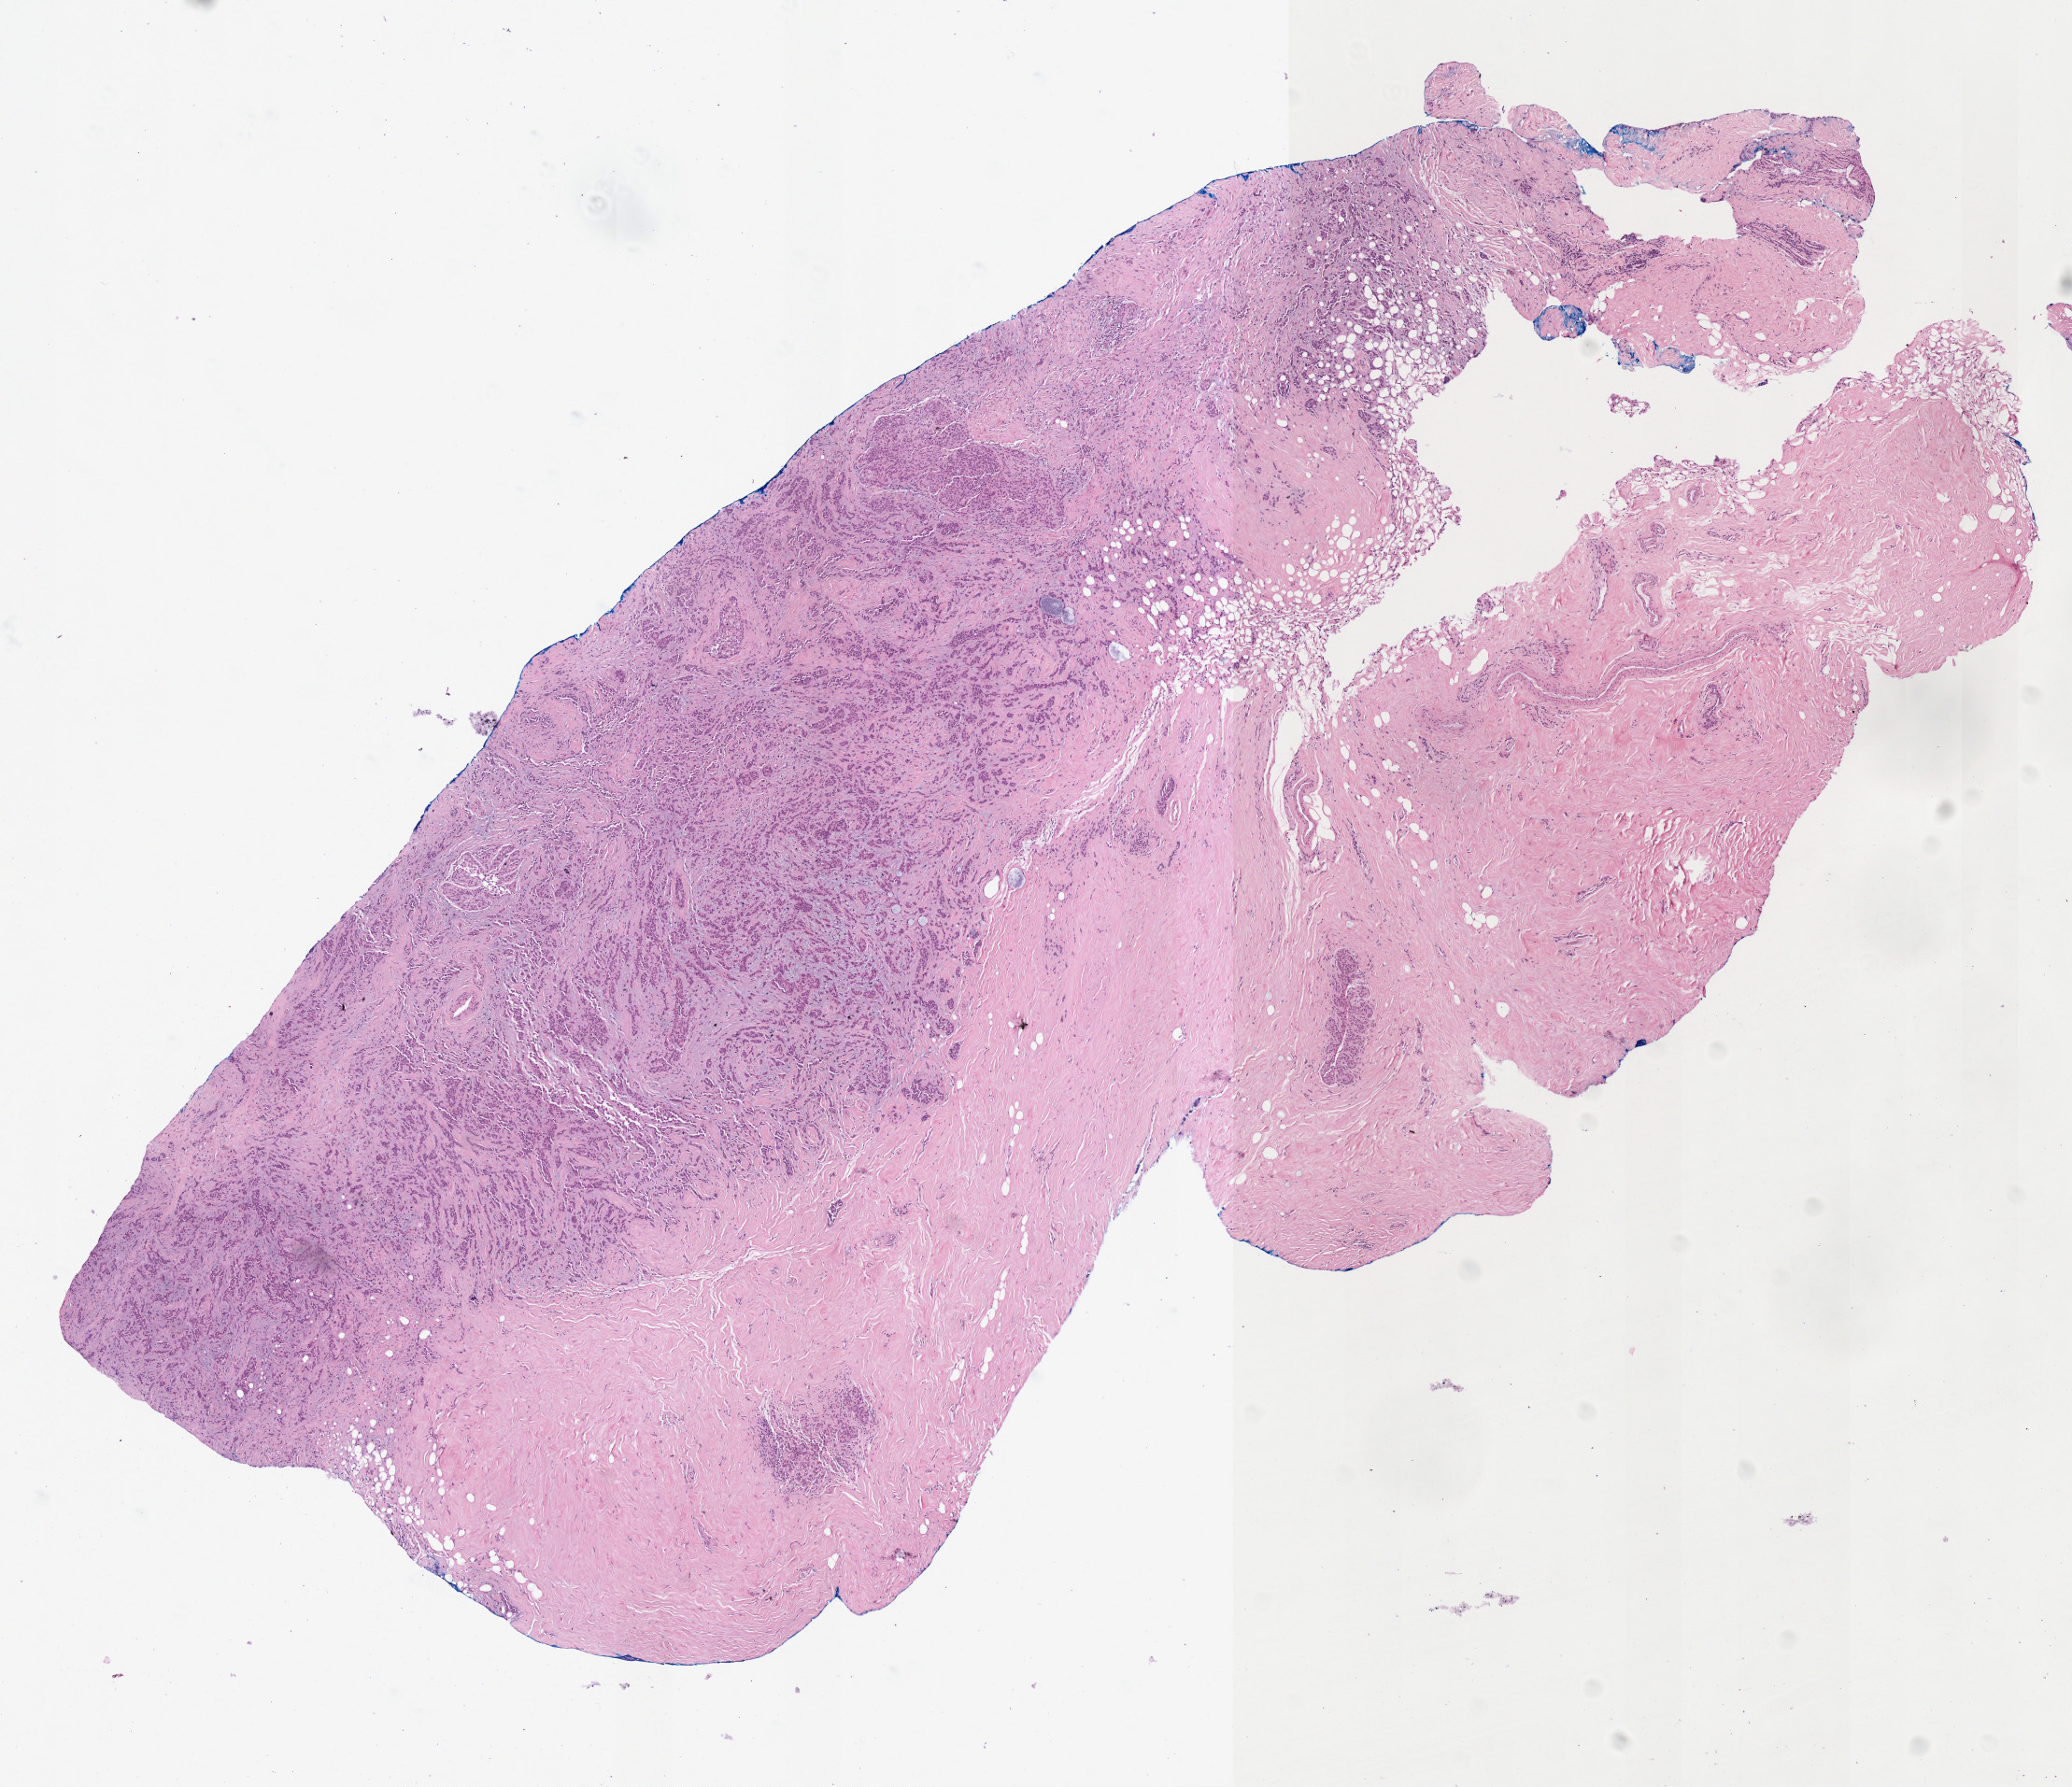
H&E whole-slide image — a low-resolution overview of the entire scanned area, about 8.9 x 7.7 mm. FFPE section. Sample: primary tumour, breast. Female, age 53 years at initial diagnosis.
TNM: T1c N0 (i-) MX. Diagnosis: Lobular carcinoma, NOS. AJCC pathologic stage: IA (7th edition). Laterality: right.